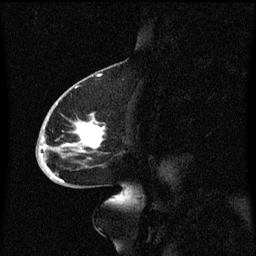
Breast MRI (dynamic contrast-enhanced), one sagittal slice. Position 31 of 60 along the scan axis. Dynamic contrast-enhanced series, image 2 of 3 at this slice position (ordered by acquisition). 1.5 T. TE 4.2 ms, TR 8.4 ms. 2 mm slice thickness. 256 × 256 image matrix. Female patient, age 68 years. From the clinical record (not read from this slice): setting: breast cancer imaged before/during neoadjuvant chemotherapy; receptor status: triple-negative.
Outlined on this slice (semi-automatically segmented with operator editing):
- analysis volume of interest (the breast-tissue region the enhancement analysis was run in; not a lesion): bounding box <37,94,120,173> (left, top, right, bottom; pixels)
- tumour enhancement mask (voxels above the 70 % enhancement threshold inside the analysis volume of interest): <41,118,106,173>